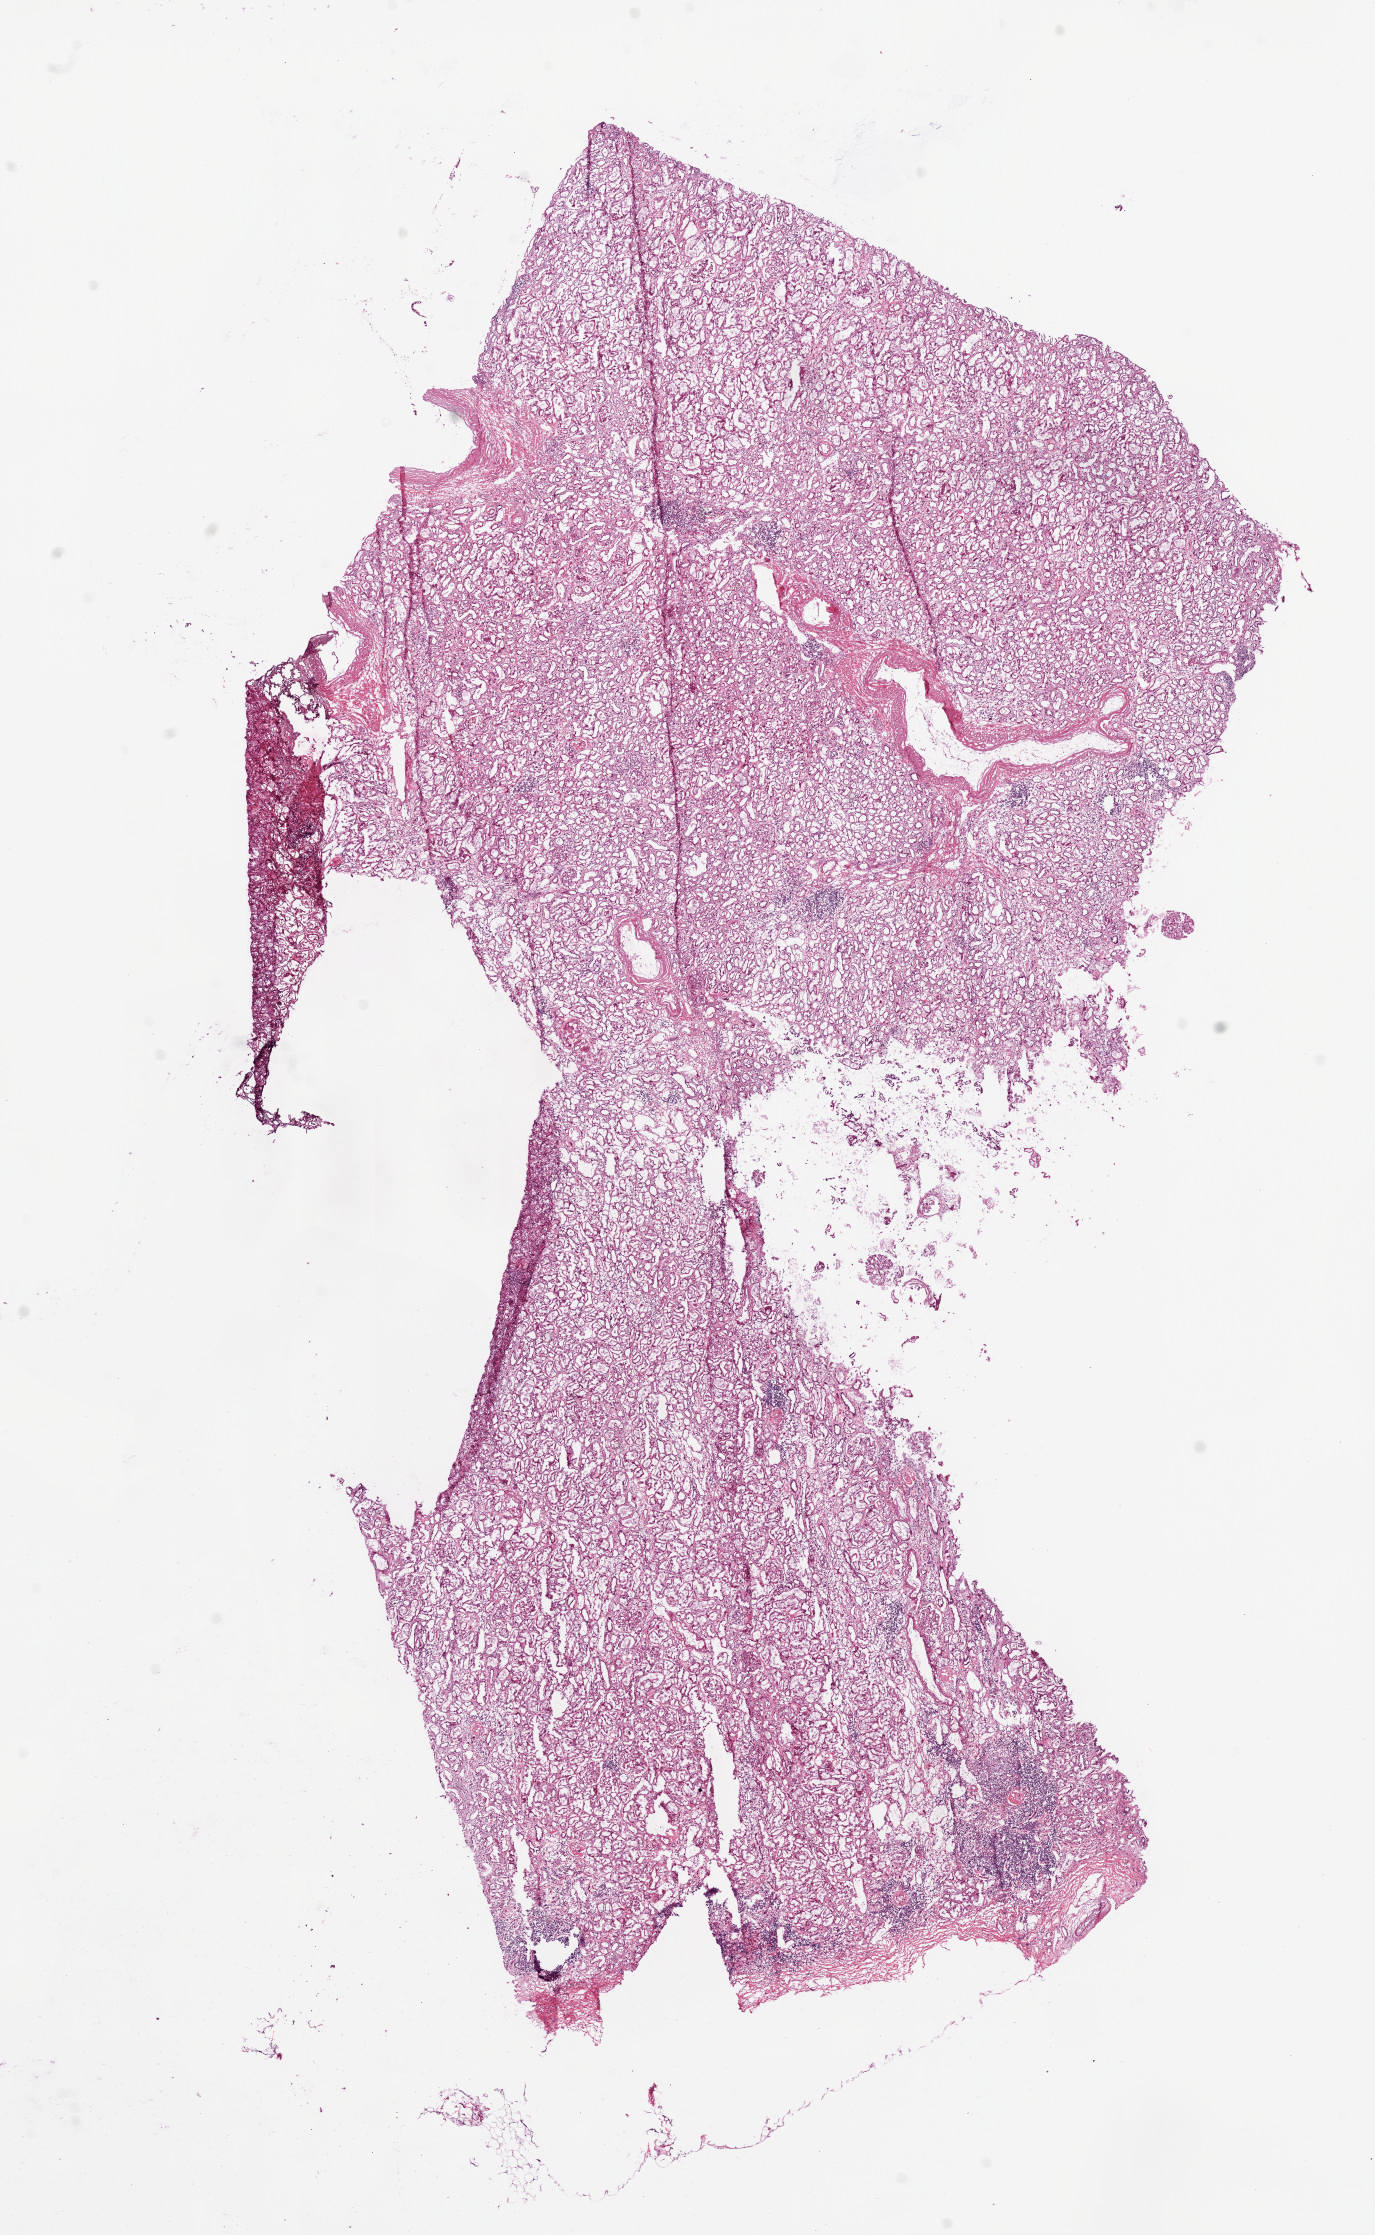
Whole-slide histology image, H&E-stained — a low-resolution overview of the entire scanned area, about 11.0 x 17.9 mm (acquisition: 20x scan). Frozen section from the bottom of the tissue portion. Solid tissue normal (non-tumour tissue) sample from the kidney. Male, age 70 years at initial diagnosis.
This section: solid tissue normal (non-tumour) sample from the same patient. Patient diagnosis: Clear cell adenocarcinoma, NOS.